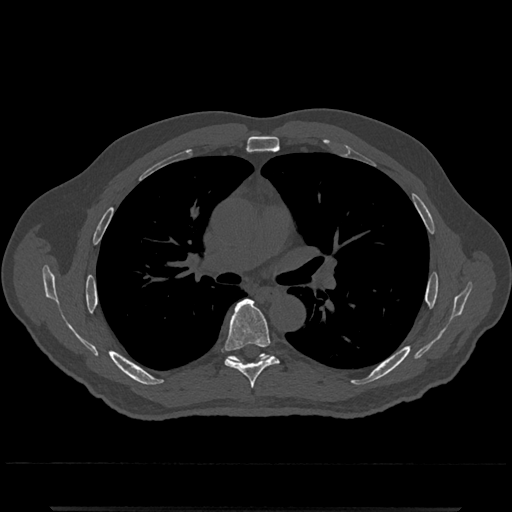
CT including the spine, one axial slice. Slice 766 of 797 in the series (ordered by position). 120 kVp. Bone window (W 1800 / L 400 HU). 0.5 mm slice thickness. 512 × 512 image matrix, field of view 393 × 393 mm. Patient: male, 67 years. From the clinical record (not read from this slice): primary cancer: prostate.
Annotated regions visible in this slice (semi-automatically segmented with operator editing):
- T6 vertebra: box from (x=222, y=299) to (x=279, y=389) px
- T7 vertebra: (x=228, y=354)–(x=271, y=363)